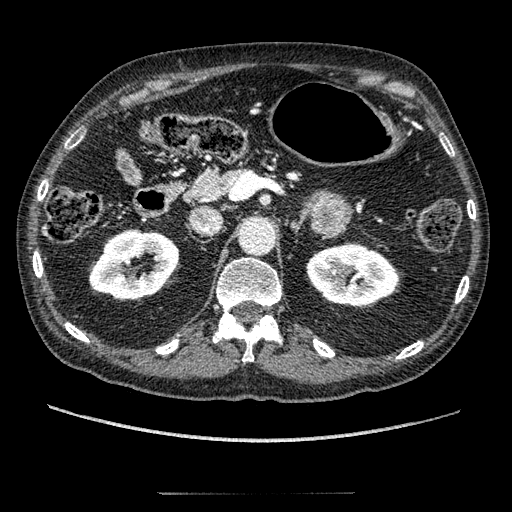
Contrast-enhanced abdominal CT, one axial slice. Position 123 of 274 along the scan axis. 120 kVp. Intravenous contrast given. Soft-tissue window (W 400 / L 40 HU). 1.25 mm slice thickness. 512 × 512 image matrix, field of view 381 × 381 mm. Male patient, age 69 years. Case-level facts recorded for this patient, not image findings: diagnosis: adrenocortical carcinoma; tumour side: left adrenal; tumour size at pathology: 6.1 cm; Ki-67 index: 10 %; stage (as recorded): 3.
Outlined on this slice (semi-automatic segmentation, software-assisted and operator-edited):
- mass: box from (x=312, y=191) to (x=350, y=234) px